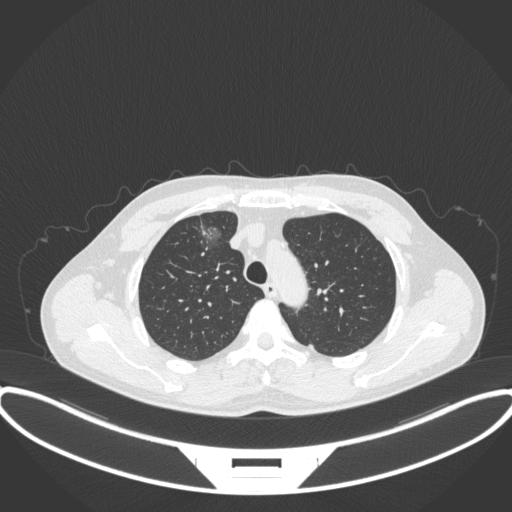
Chest CT, one axial slice. Slice 281 of 395 in the series (ordered by position). Lung window (W 1500 / L -600 HU). 1 mm slice thickness. 512 × 512 image matrix, field of view 424 × 424 mm. Male patient, age 60 years. Case-level facts recorded for this patient, not image findings: clinical TNM (as recorded): T1c N0 M0.
Structures marked on this image (rectangle marked by the reading radiologist):
- lung tumour (recorded histology: adenocarcinoma): bounding box [x1, y1, x2, y2] px = [192, 216, 230, 255]